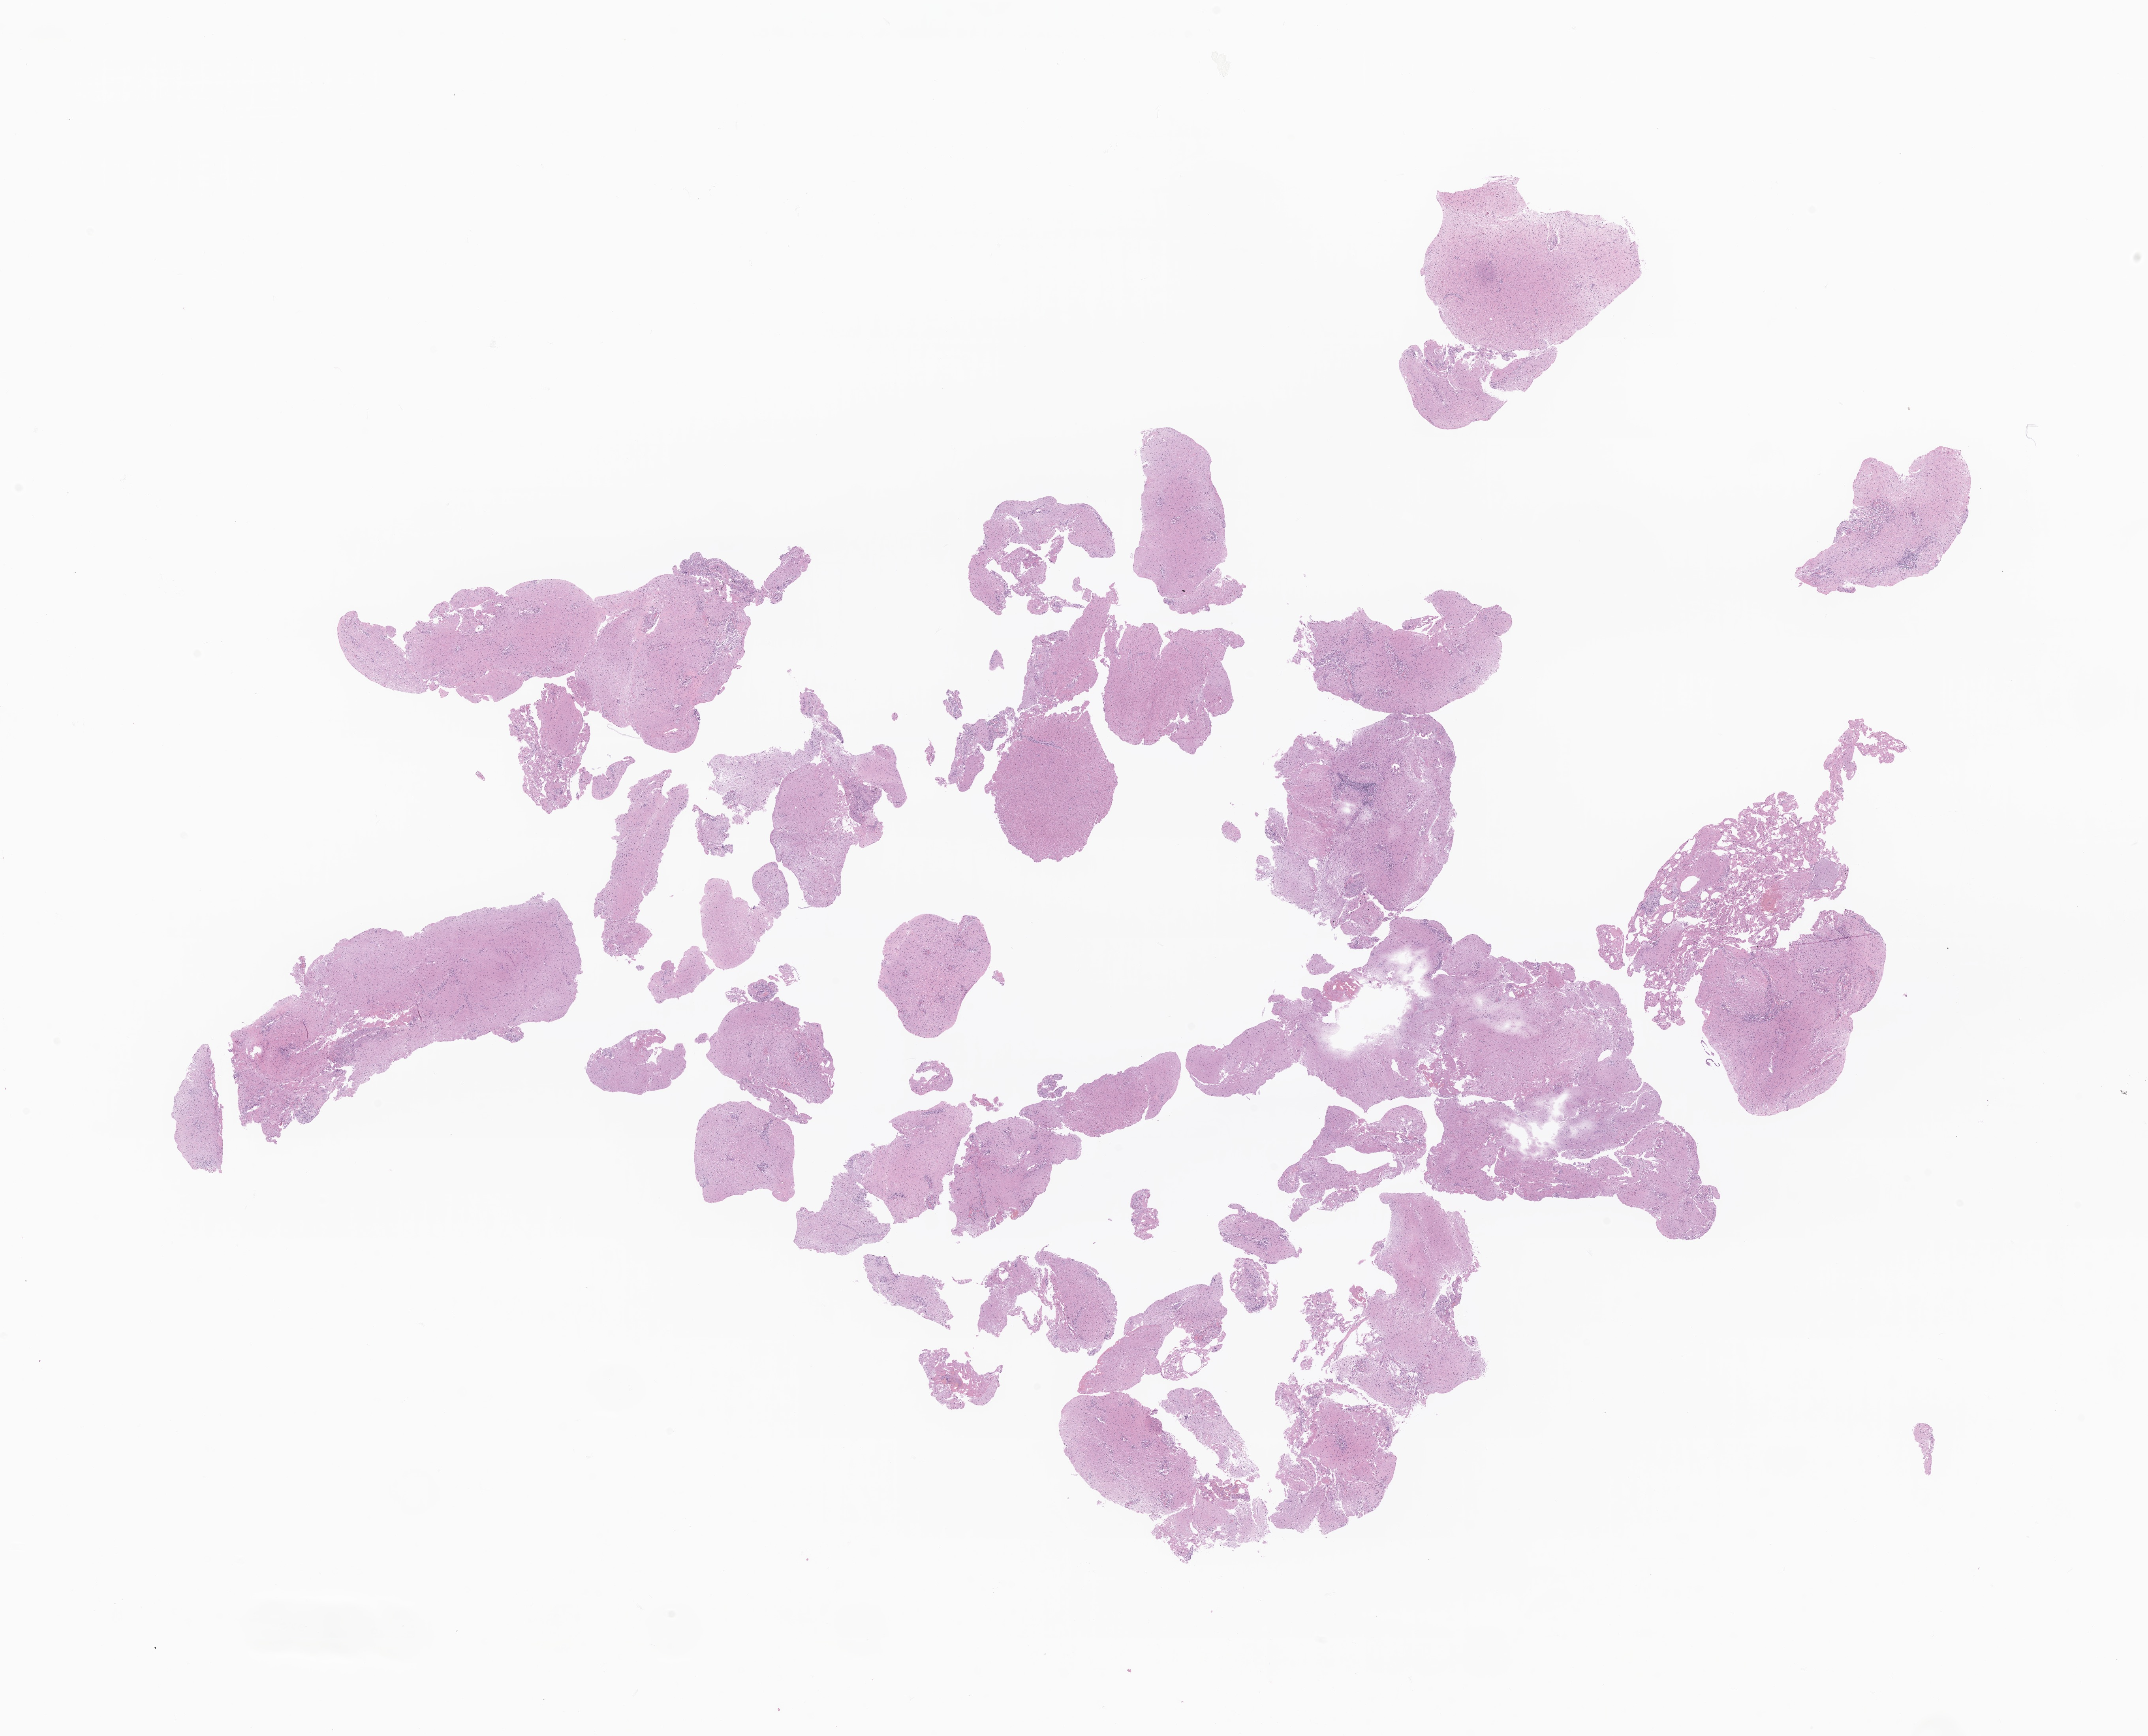
H&E whole-slide image of tumor tissue from the brain, low-resolution overview of the scanned area, about 22.9 x 18.5 mm, formalin-fixed paraffin-embedded section. Male patient, age 166 months (13 years 10 months).
Recorded diagnosis: Pilocytic astrocytoma.